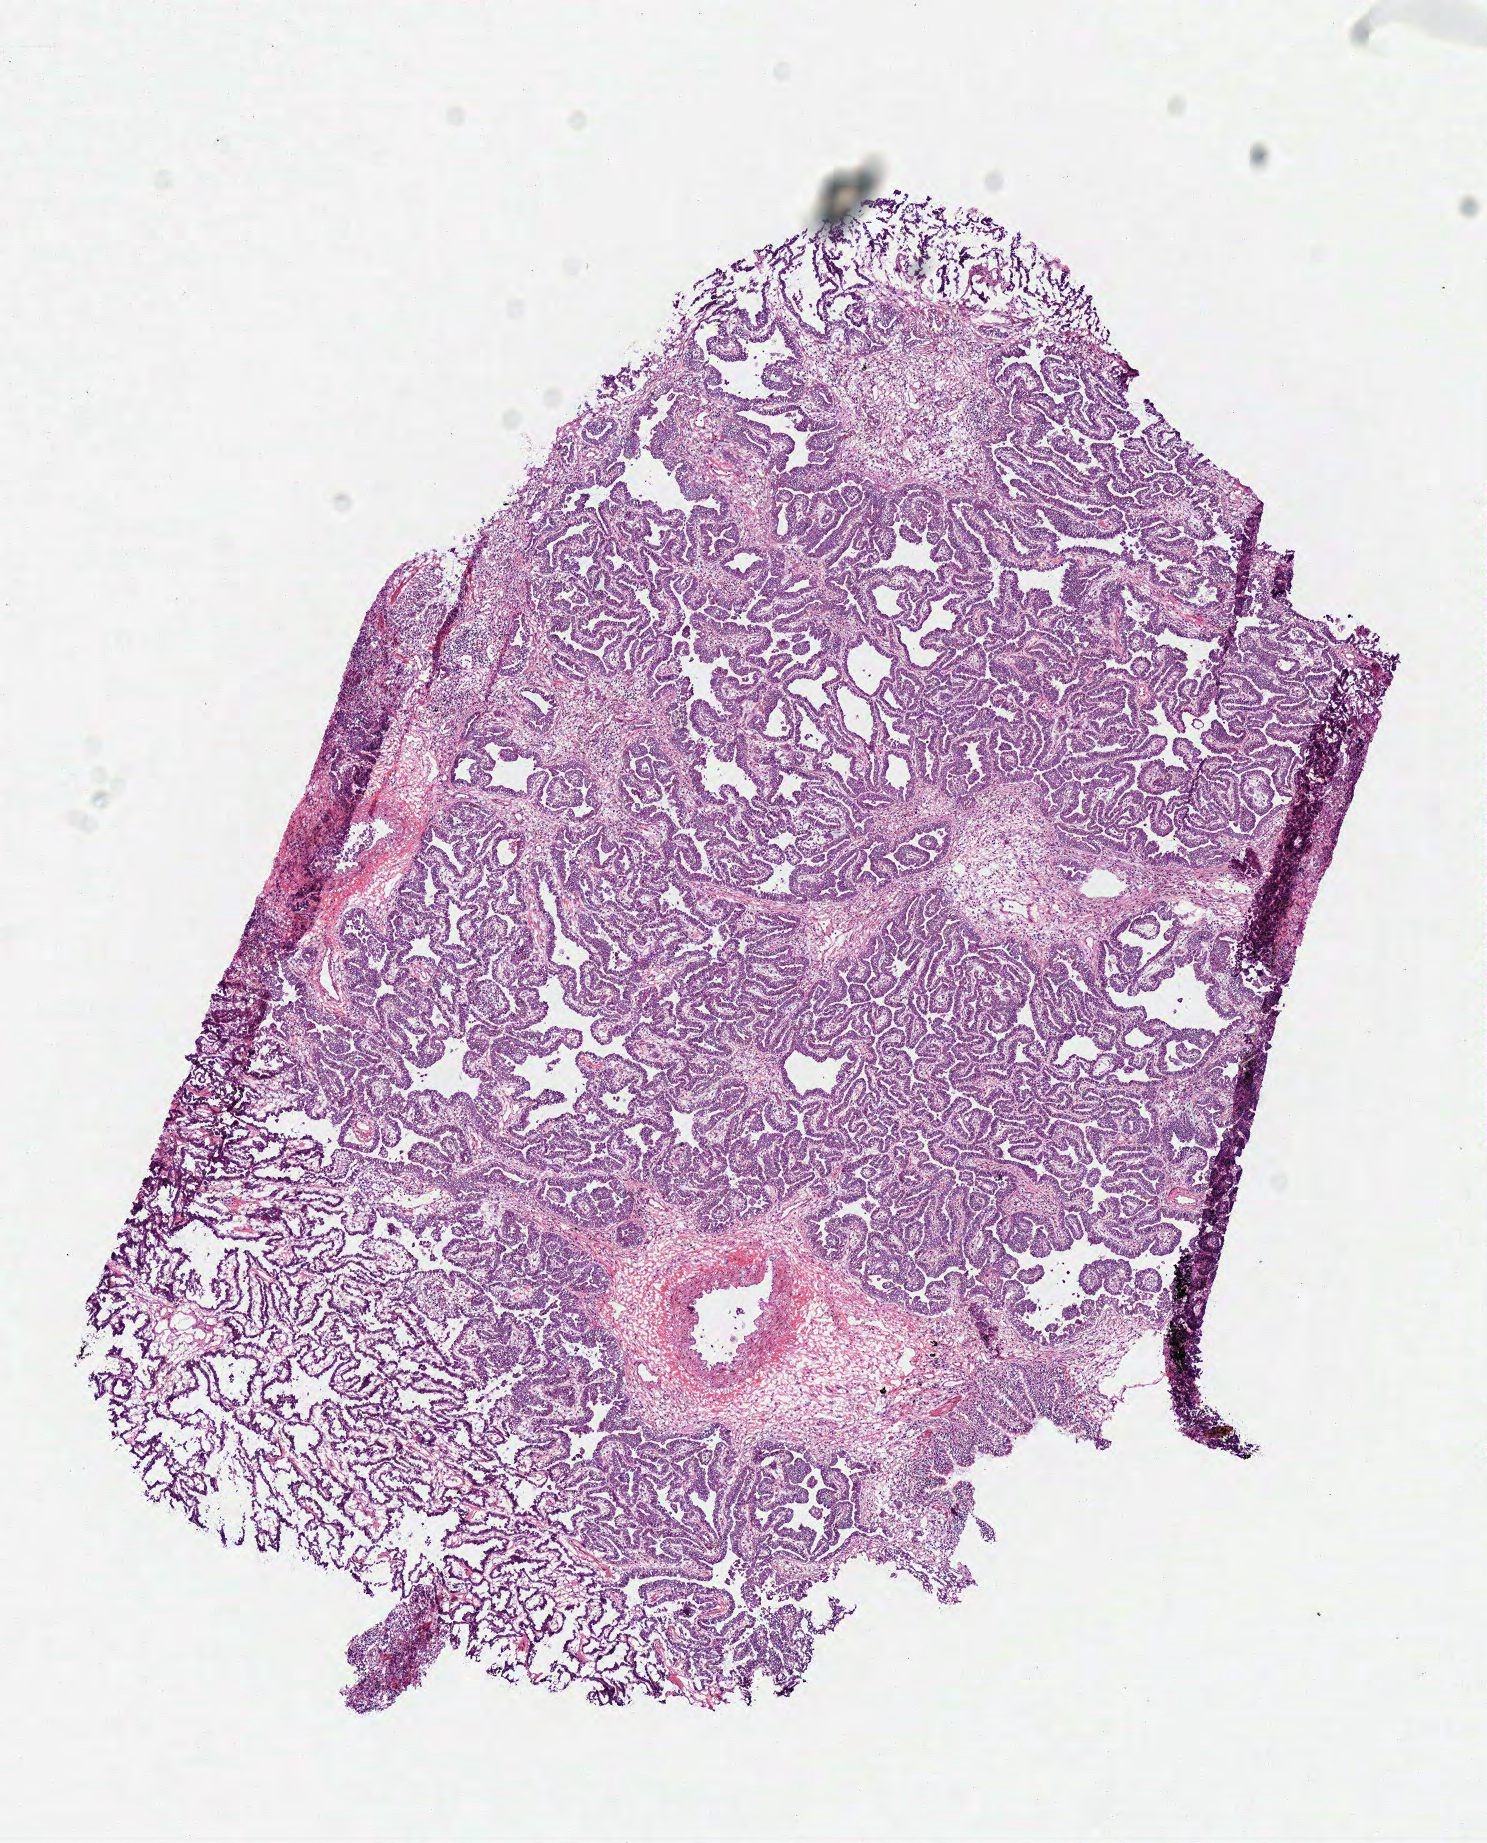
Digitized H&E-stained tissue section (whole slide) — low-resolution overview of the scanned area, about 5.9 x 7.3 mm (slide scanned at 40x); frozen section from the top of the tissue portion; primary tumour sample from the lung. Male, age 77 years at initial diagnosis. Pathologist review of this section (percent, as recorded): tumour cells 85%, tumour nuclei 75%, normal cells 0%, stromal cells 15%, necrosis 0%.
AJCC pathologic stage: IV. Histologic diagnosis: Papillary adenocarcinoma, NOS. TNM: T2 N0 M1.